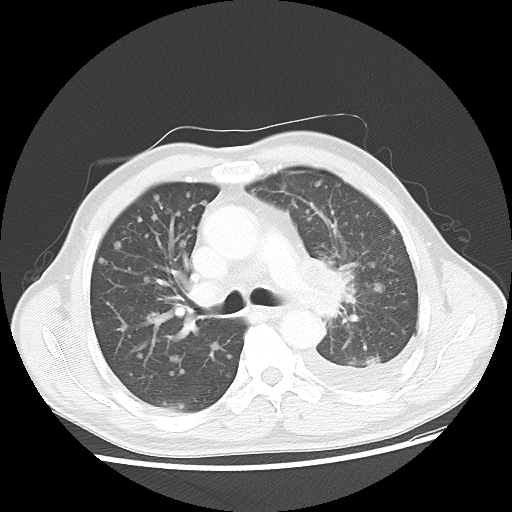
Chest CT, one axial slice; position 29 of 47 along the scan axis; reconstruction kernel LUNG; 100 kVp; lung window (W 1500 / L -600 HU); 5 mm slice thickness; 512 × 512 image matrix, field of view 362 × 362 mm. Male patient, age 55 years. Case-level facts recorded for this patient, not image findings: clinical TNM (as recorded): T2 N3 M1a; histopathological grade: G3.
Annotated regions visible in this slice (rectangle marked by the reading radiologist):
- lung tumour (recorded histology: squamous cell carcinoma): bounding box [x1, y1, x2, y2] px = [312, 245, 366, 337]